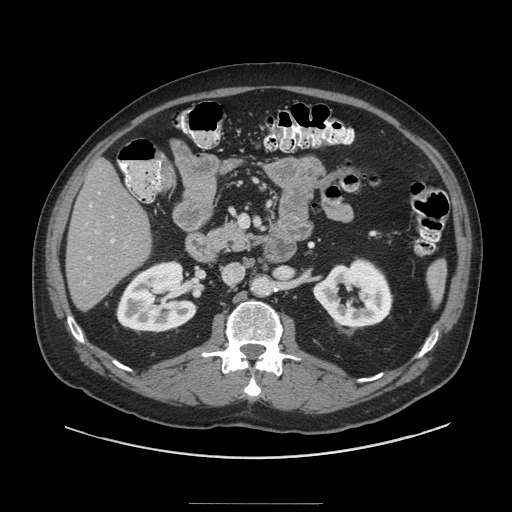
Contrast-enhanced abdominal CT (liver protocol), one axial slice; position 38 of 91 along the scan axis; reconstruction kernel STANDARD; 140 kVp; soft-tissue window (W 400 / L 40 HU); 2.5 mm slice thickness; 512 × 512 image matrix, field of view 440 × 440 mm. From the clinical record (not read from this slice): diagnosis: hepatocellular carcinoma (patient treated with transarterial chemoembolisation; whether this scan precedes or follows treatment is not stated here); TNM stage (as recorded): Stage-I; Child-Pugh class: A; tumour differentiation: well differentiated; tumour nodularity: uninodular.
Outlined on this slice (semi-automatically segmented with operator editing):
- liver parenchyma outside the tumour (the mass and vessels are separate outlines, so this box may not span the whole liver): bounding box <66,160,150,310> (left, top, right, bottom; pixels)
- liver vessels: <86,192,115,260>